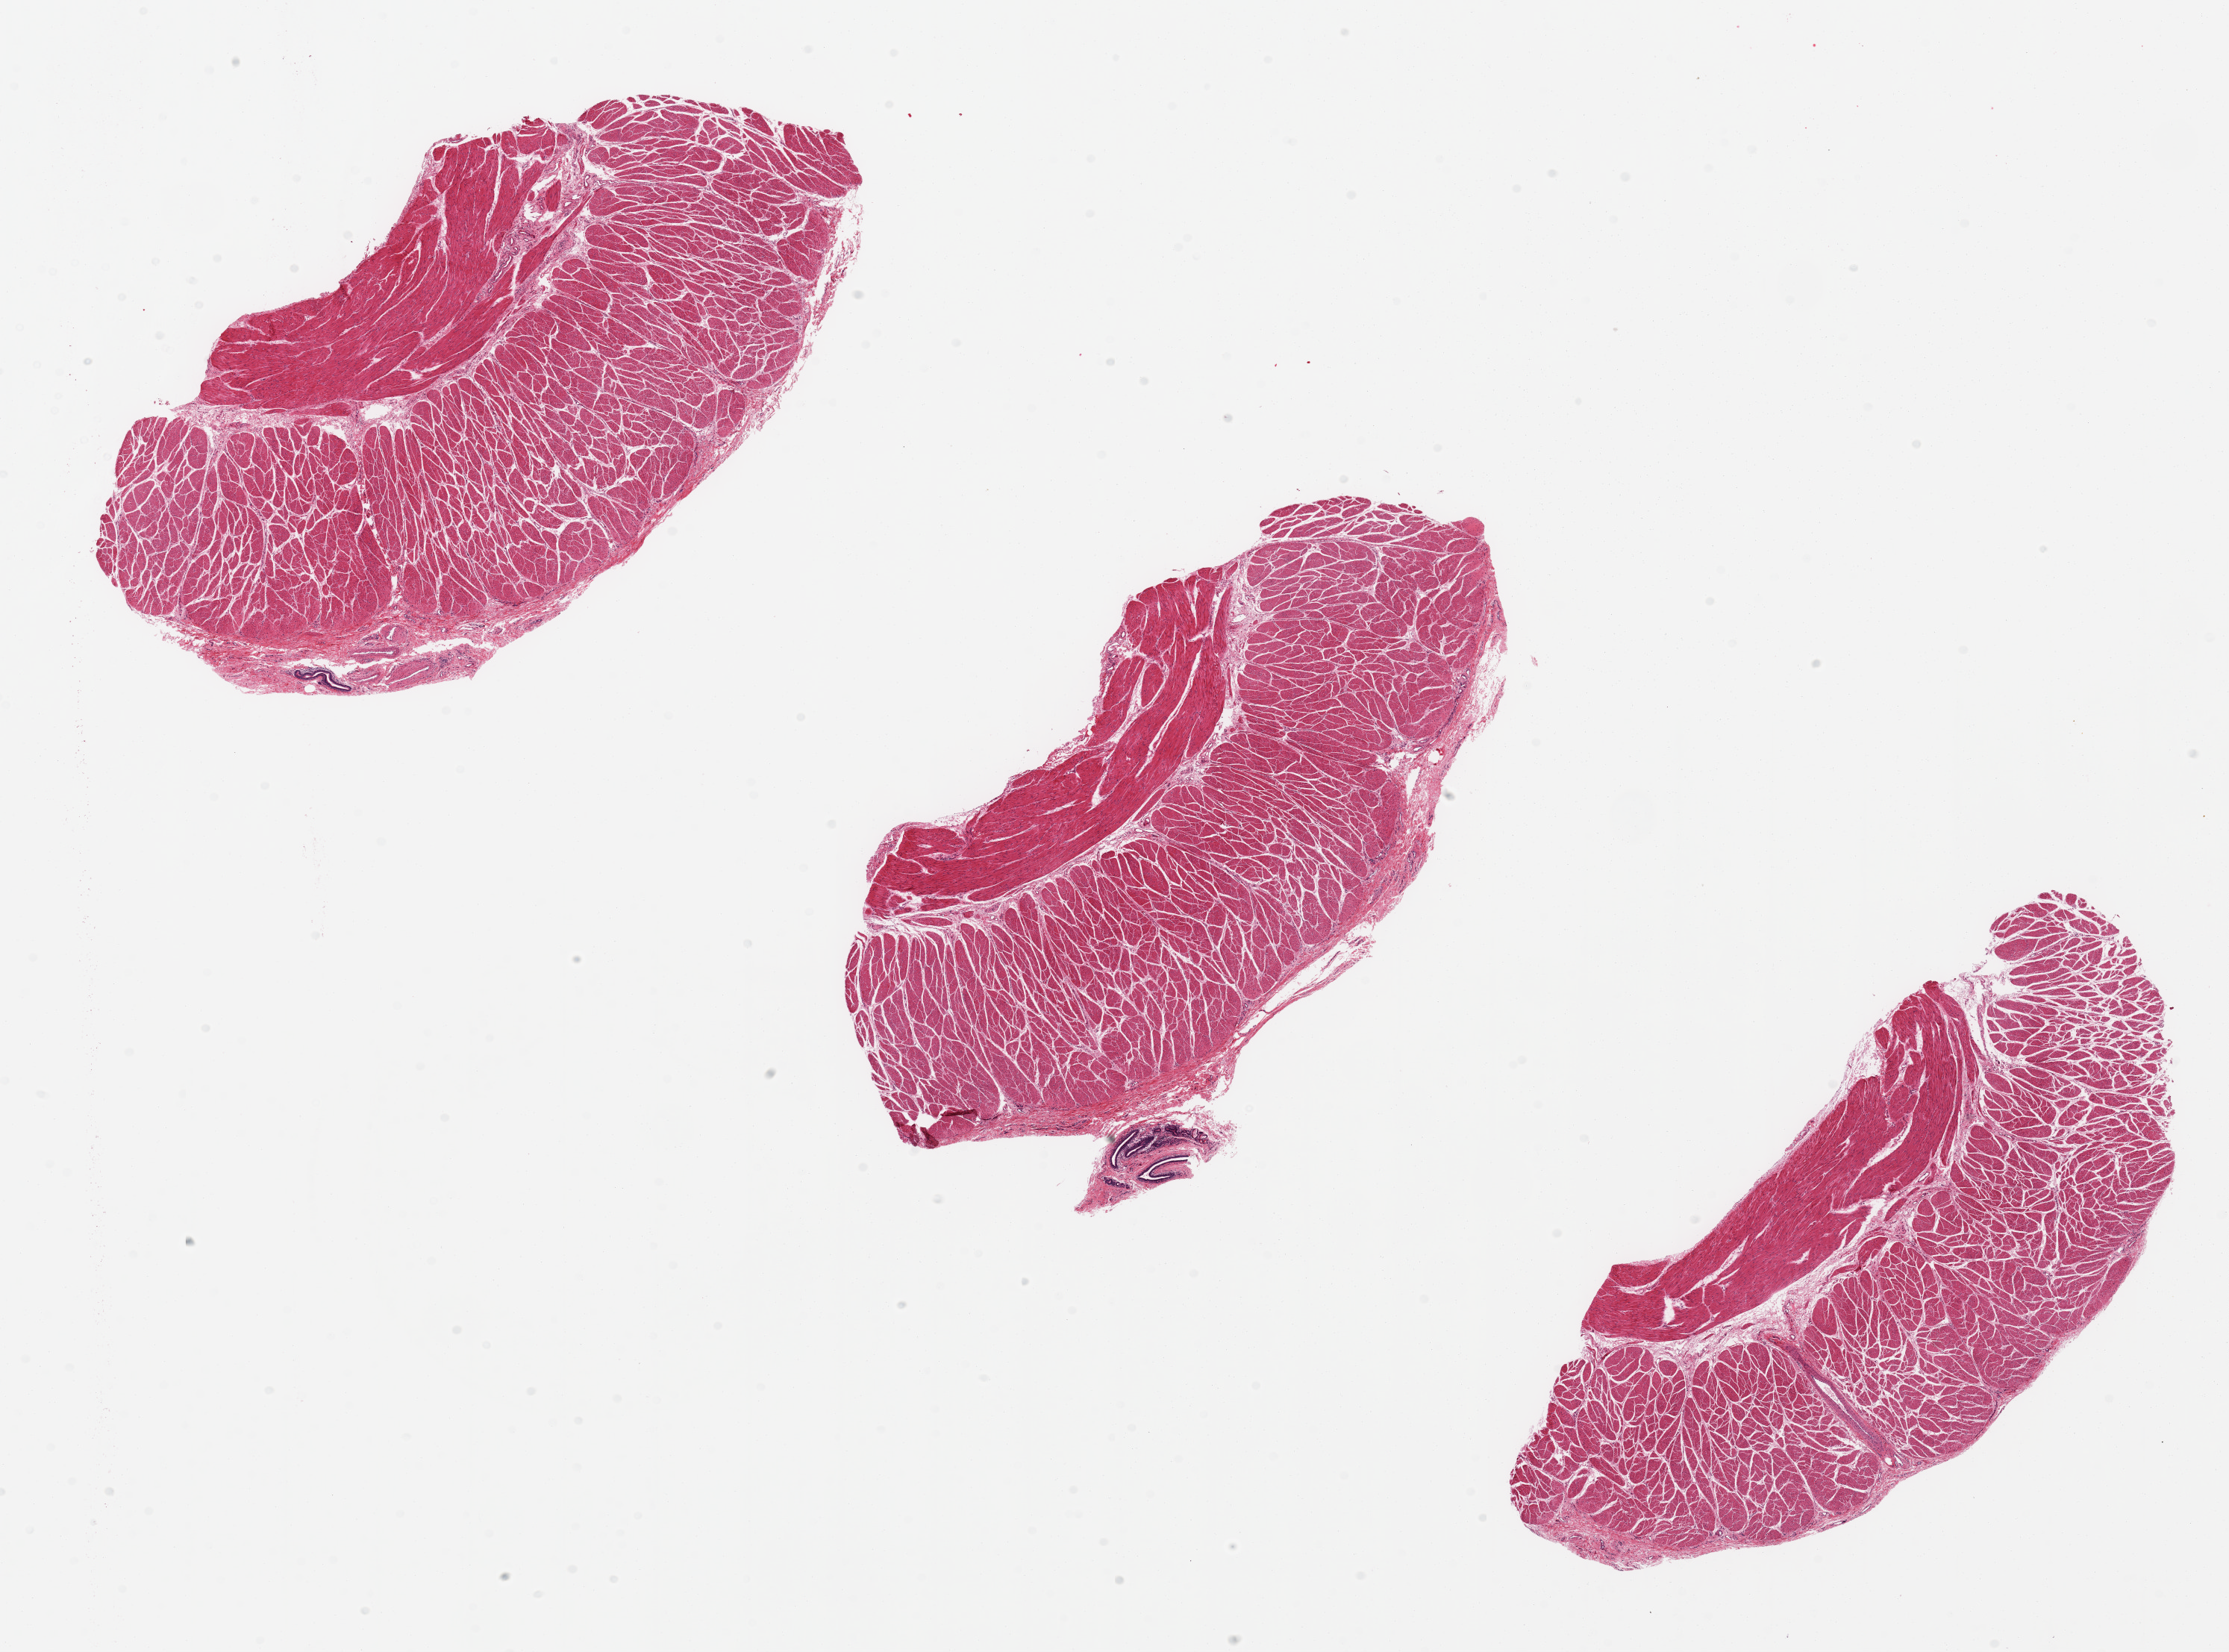
Digitized haematoxylin and eosin-stained section — whole scanned area (about 23.6 x 17.5 mm, from a 20x scan) shown as a low-resolution overview; PAXgene-fixed paraffin-embedded (PFPE) section; target tissue: esophageal muscle; donor tissue sample.
Pathologist's review note for this sample: 3 ~8.5x3.5mm pieces; small floater of ?bronchial mucosa.